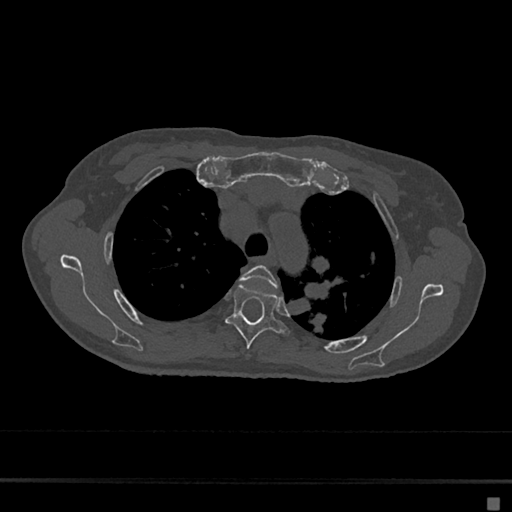
CT including the spine, one axial slice; position 506 of 797 along the scan axis; 120 kVp; bone window (W 1800 / L 400 HU); 512 × 512 image matrix. Patient: female, 68 years. From the clinical record (not read from this slice): primary cancer: renal.
Outlined on this slice (semi-automatically segmented with operator editing):
- T3 vertebra: bounding box [x1, y1, x2, y2] px = [240, 265, 278, 288]
- T4 vertebra: [225, 283, 289, 348]